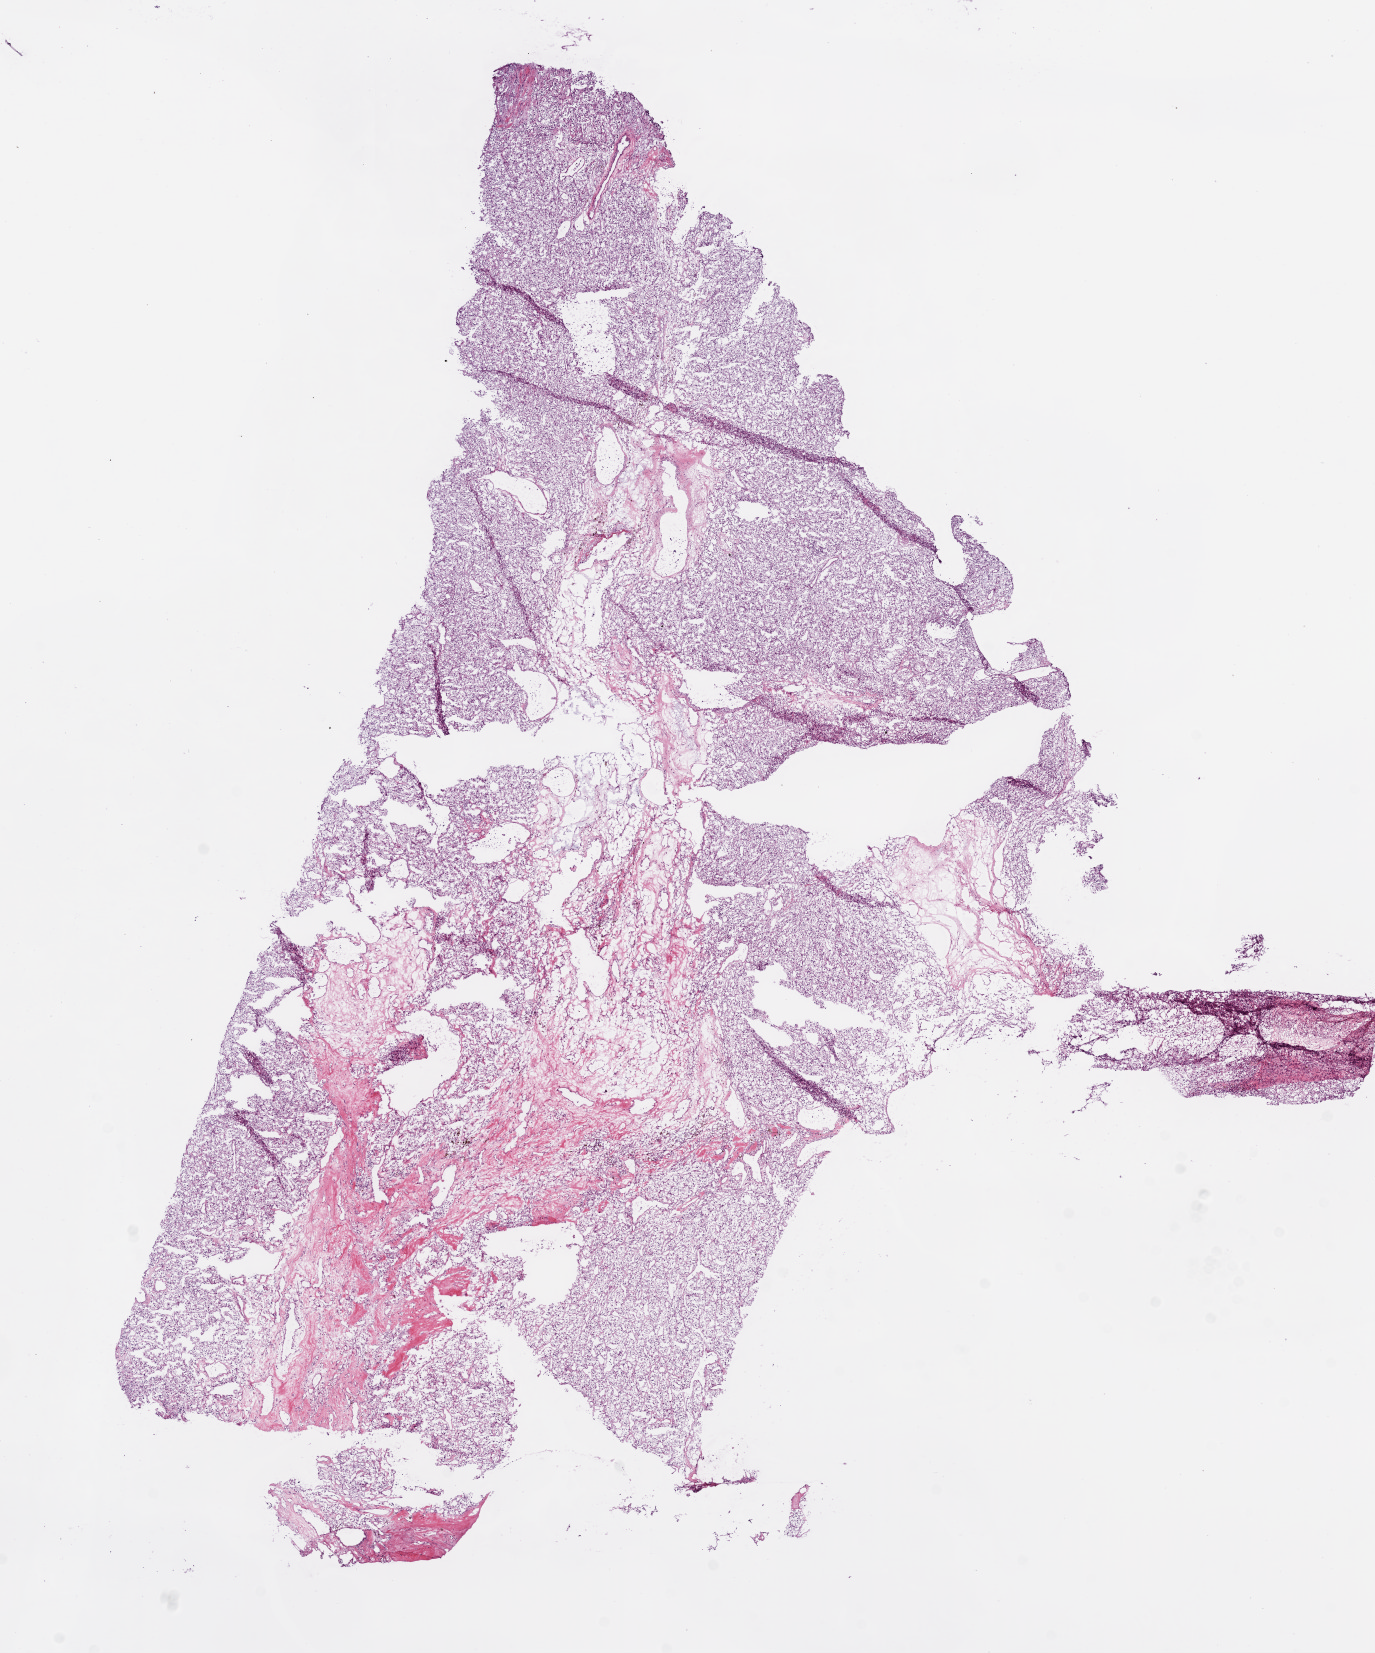
Digitized H&E tissue section (whole slide), low-resolution overview of the scanned area, about 11.0 x 13.3 mm (from a 20x scan), frozen section from the bottom of the tissue portion, kidney, primary tumour sample. Male, age 79 years at initial diagnosis. Histologic grade: G3 (poorly differentiated). Slide review estimates, as recorded: tumour cells 85%, tumour nuclei 90%, normal cells 0%, stromal cells 15%, necrosis 0%.
* pathologic diagnosis: Clear cell adenocarcinoma, NOS
* AJCC pathologic stage: III